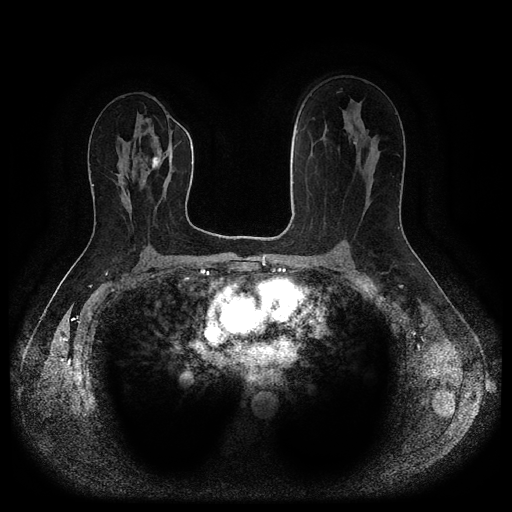
Breast MRI (dynamic contrast-enhanced, multi-phase), one axial slice. Slice 58 of 116 in the series (ordered by position). Dynamic contrast-enhanced series, time point 2 of 5 at this slice position (early post-contrast). 1.5 T. TE 2.6 ms, TR 5.3 ms. 2.2 mm slice thickness. 512 × 512 image matrix, field of view 360 × 360 mm. Female patient, age 53 years.
Structures marked on this image (semi-automatic segmentation, software-assisted and operator-edited):
- breast lesion (labelled benign in the annotation): bounding box <152,157,161,168> (left, top, right, bottom; pixels)